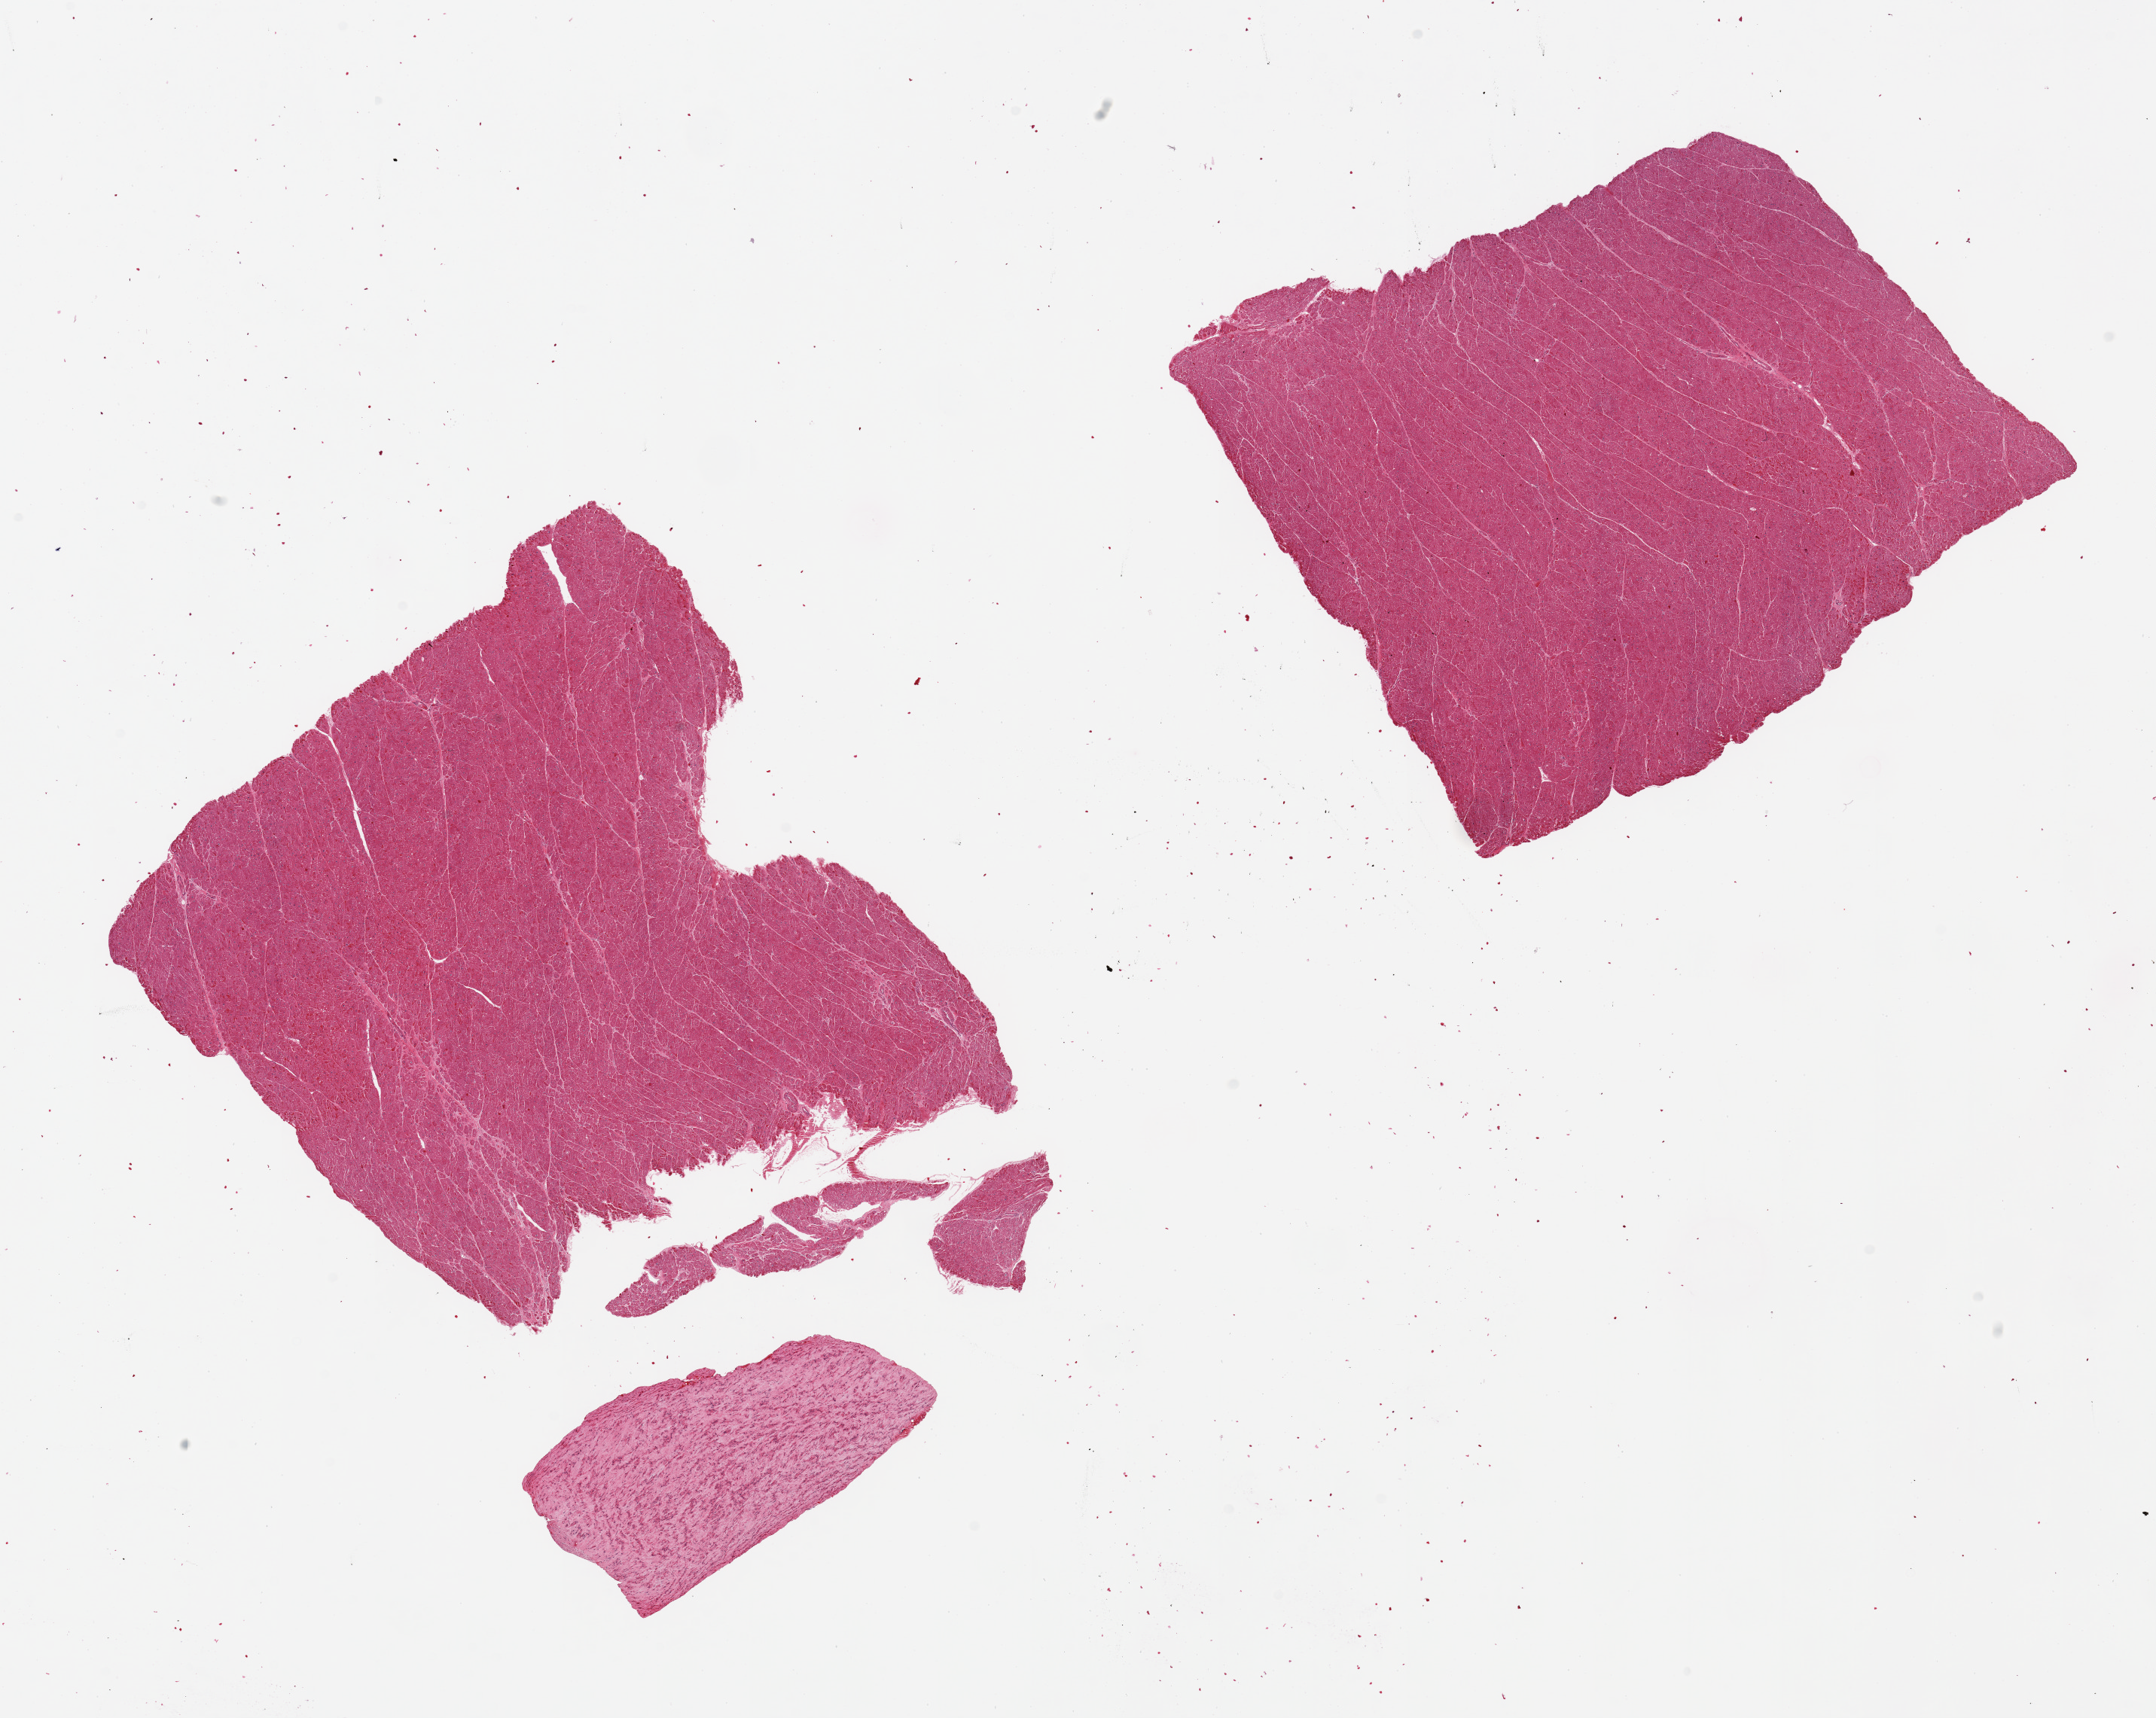
Whole-slide image, H&E stain — shown as a low-resolution overview of the whole scanned area (about 22.6 x 18.0 mm); PAXgene-fixed paraffin-embedded (PFPE) section; target tissue: heart; donor tissue sample. Male donor.
Review note (as recorded): 2 pieces and small fragment of ?pericardium (not target).